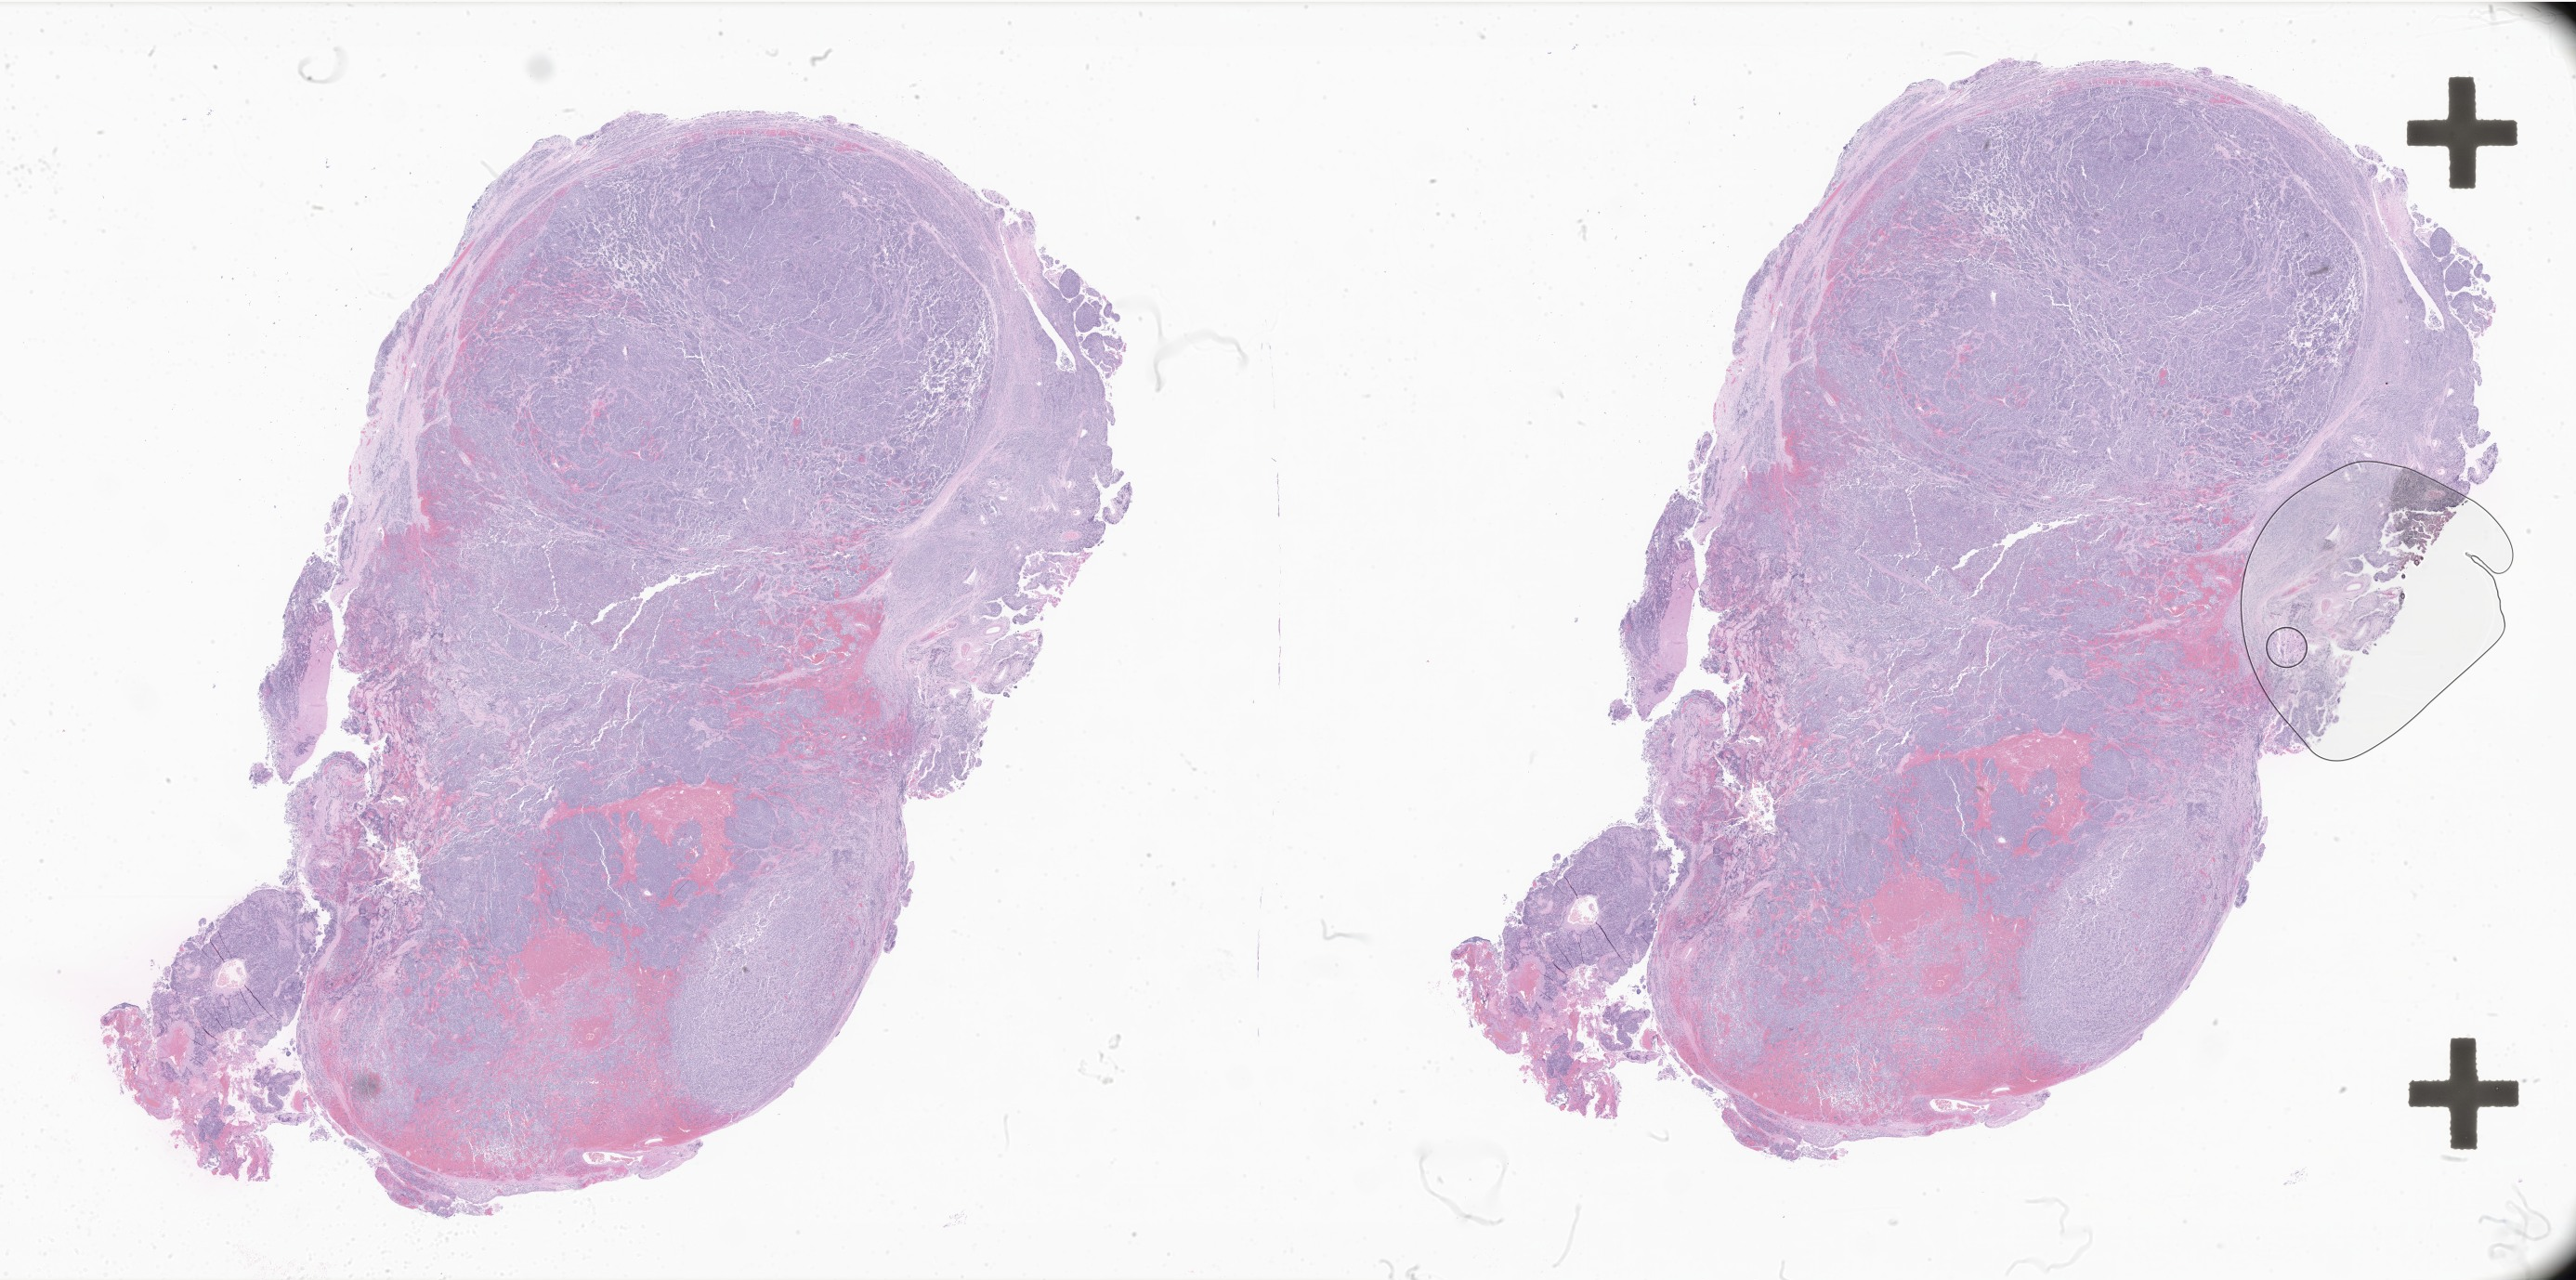
Digitized H&E-stained section of tumor tissue from the brain — a low-resolution overview of the entire scanned area, about 46.8 x 23.2 mm, FFPE section. Patient male; age 88 months.
Diagnosis: Neuroepithelioma, NOS.